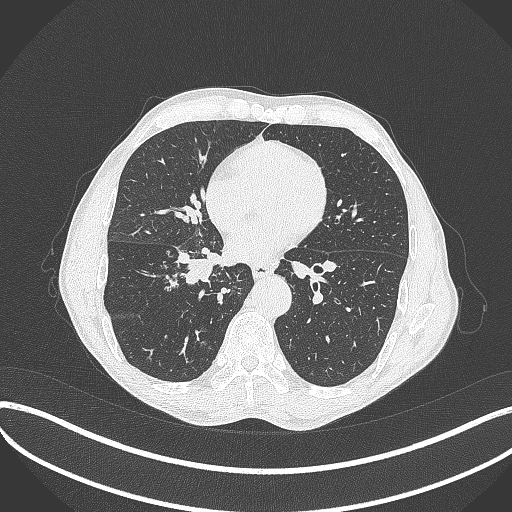
Chest CT, one axial slice; position 188 of 481 along the scan axis; reconstruction kernel B70f; 120 kVp; lung window (W 1500 / L -600 HU); 1 mm slice thickness; 512 × 512 image matrix, field of view 400 × 400 mm. Male patient, age 65 years. Case-level facts recorded for this patient, not image findings: clinical TNM (as recorded): T2a N0 M0.
Structures marked on this image (rectangle marked by the reading radiologist):
- lung tumour (recorded histology: squamous cell carcinoma): bounding box [x1, y1, x2, y2] px = [174, 245, 225, 286]